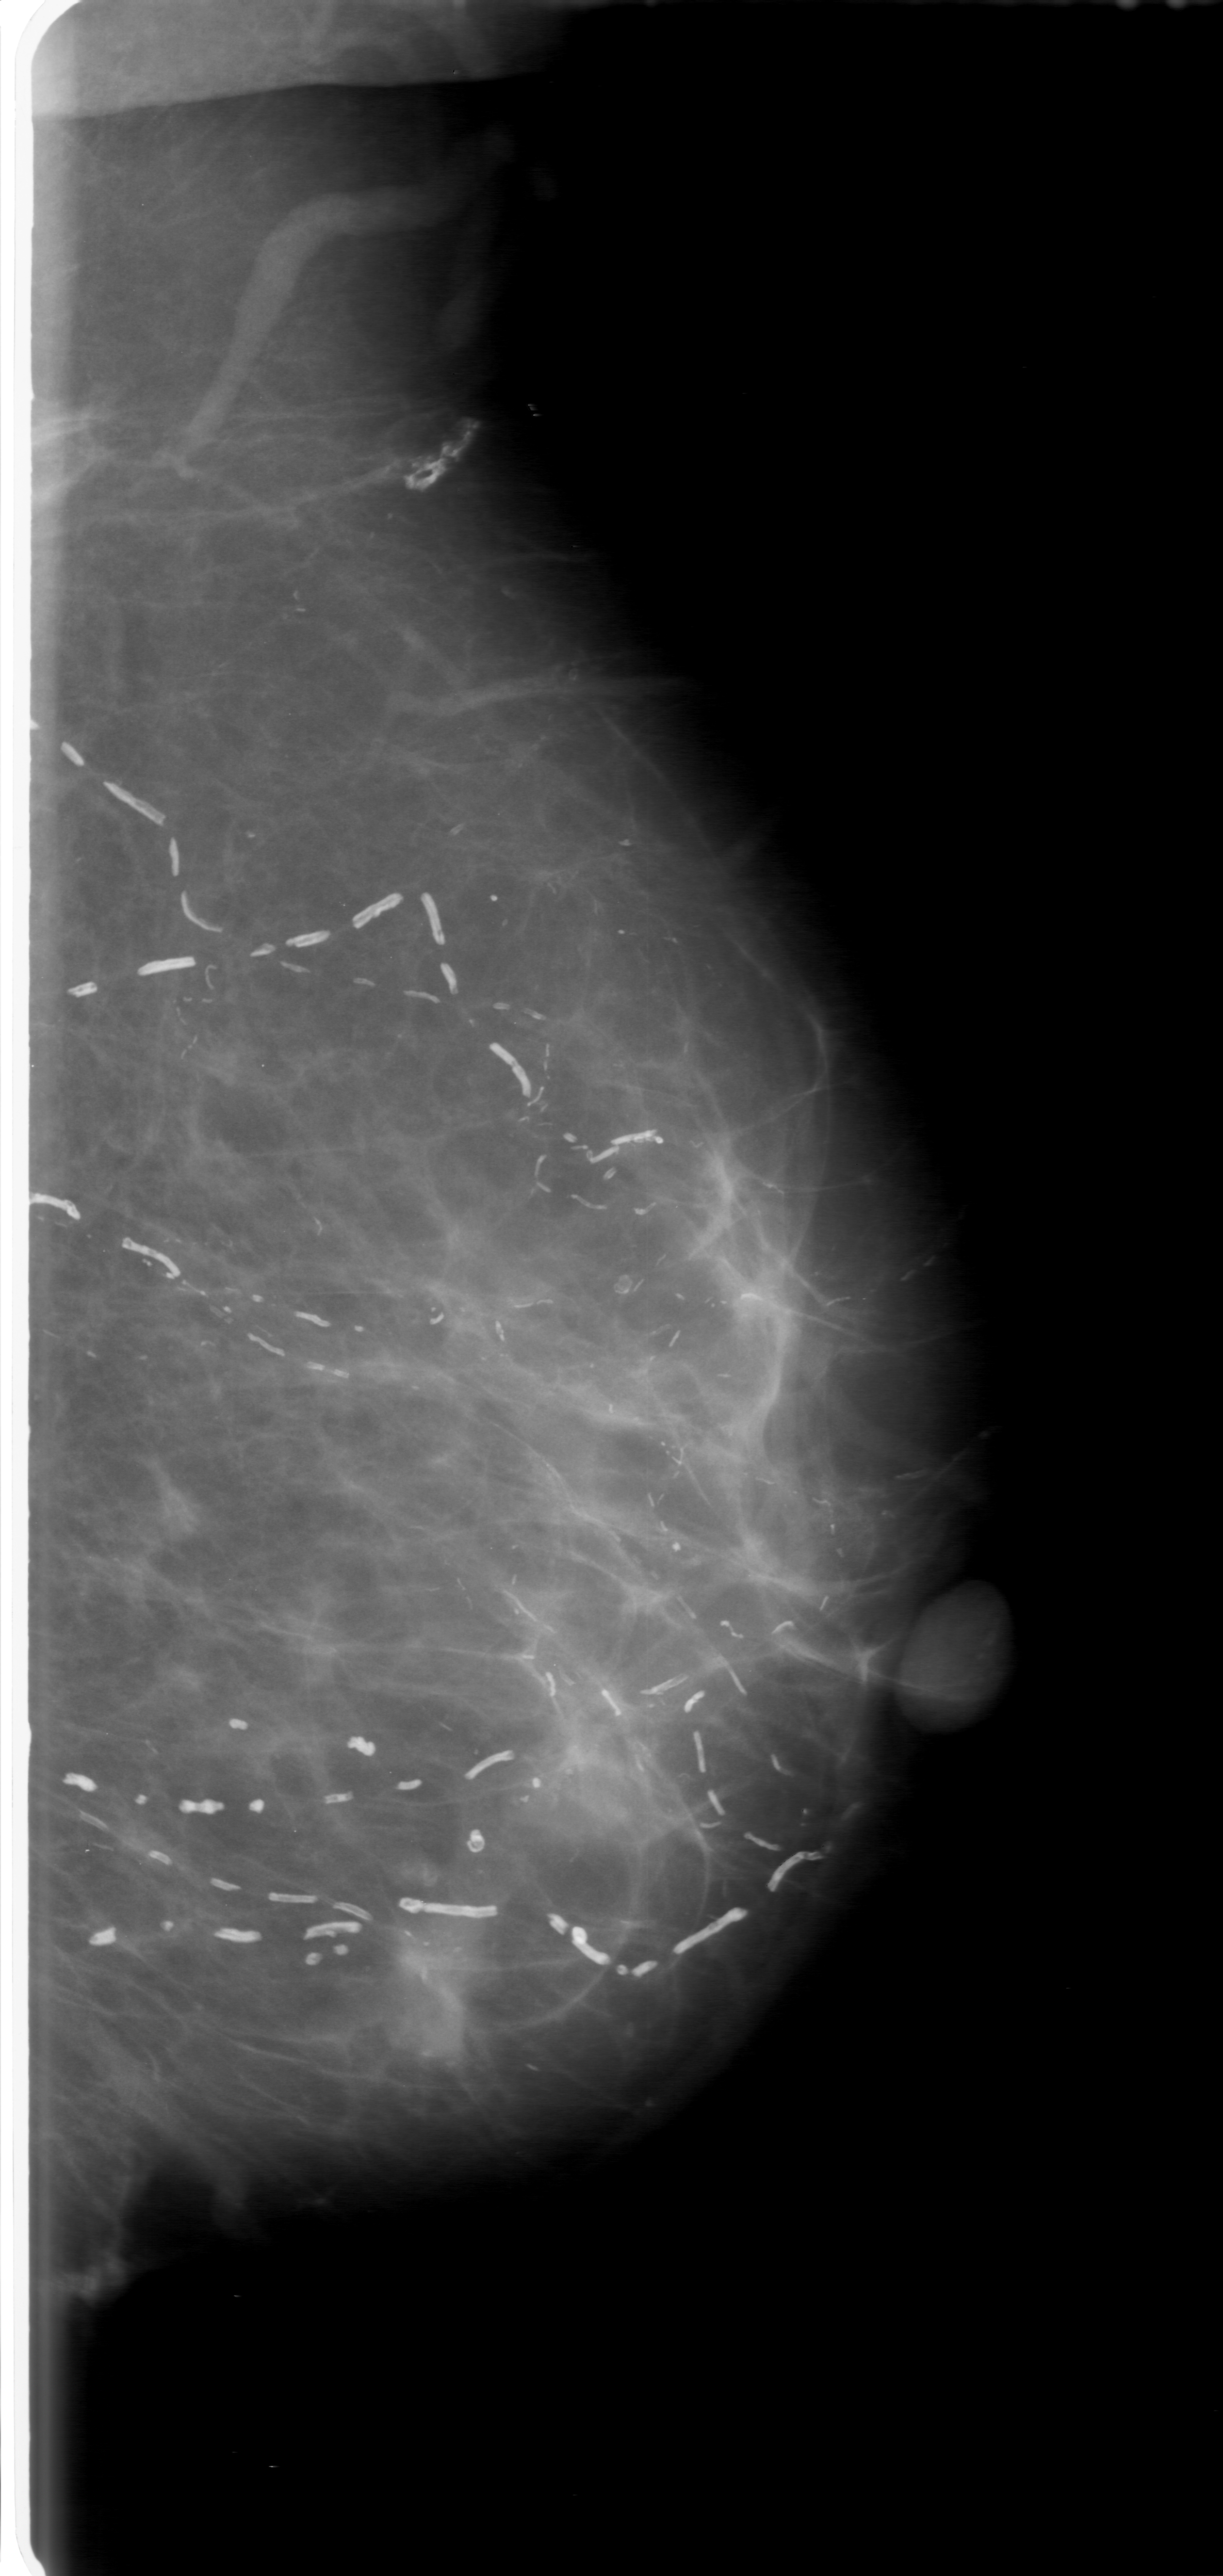
Scanned film-screen mammogram; left breast; MLO view; BI-RADS breast density category 2 (scale 1–4).
Finding: mass, shape irregular, margins ill defined; BI-RADS assessment category 3; subtlety rating 3 on a 1 (subtle) to 5 (obvious) scale; pathology result (as recorded, not read from the image): malignant.